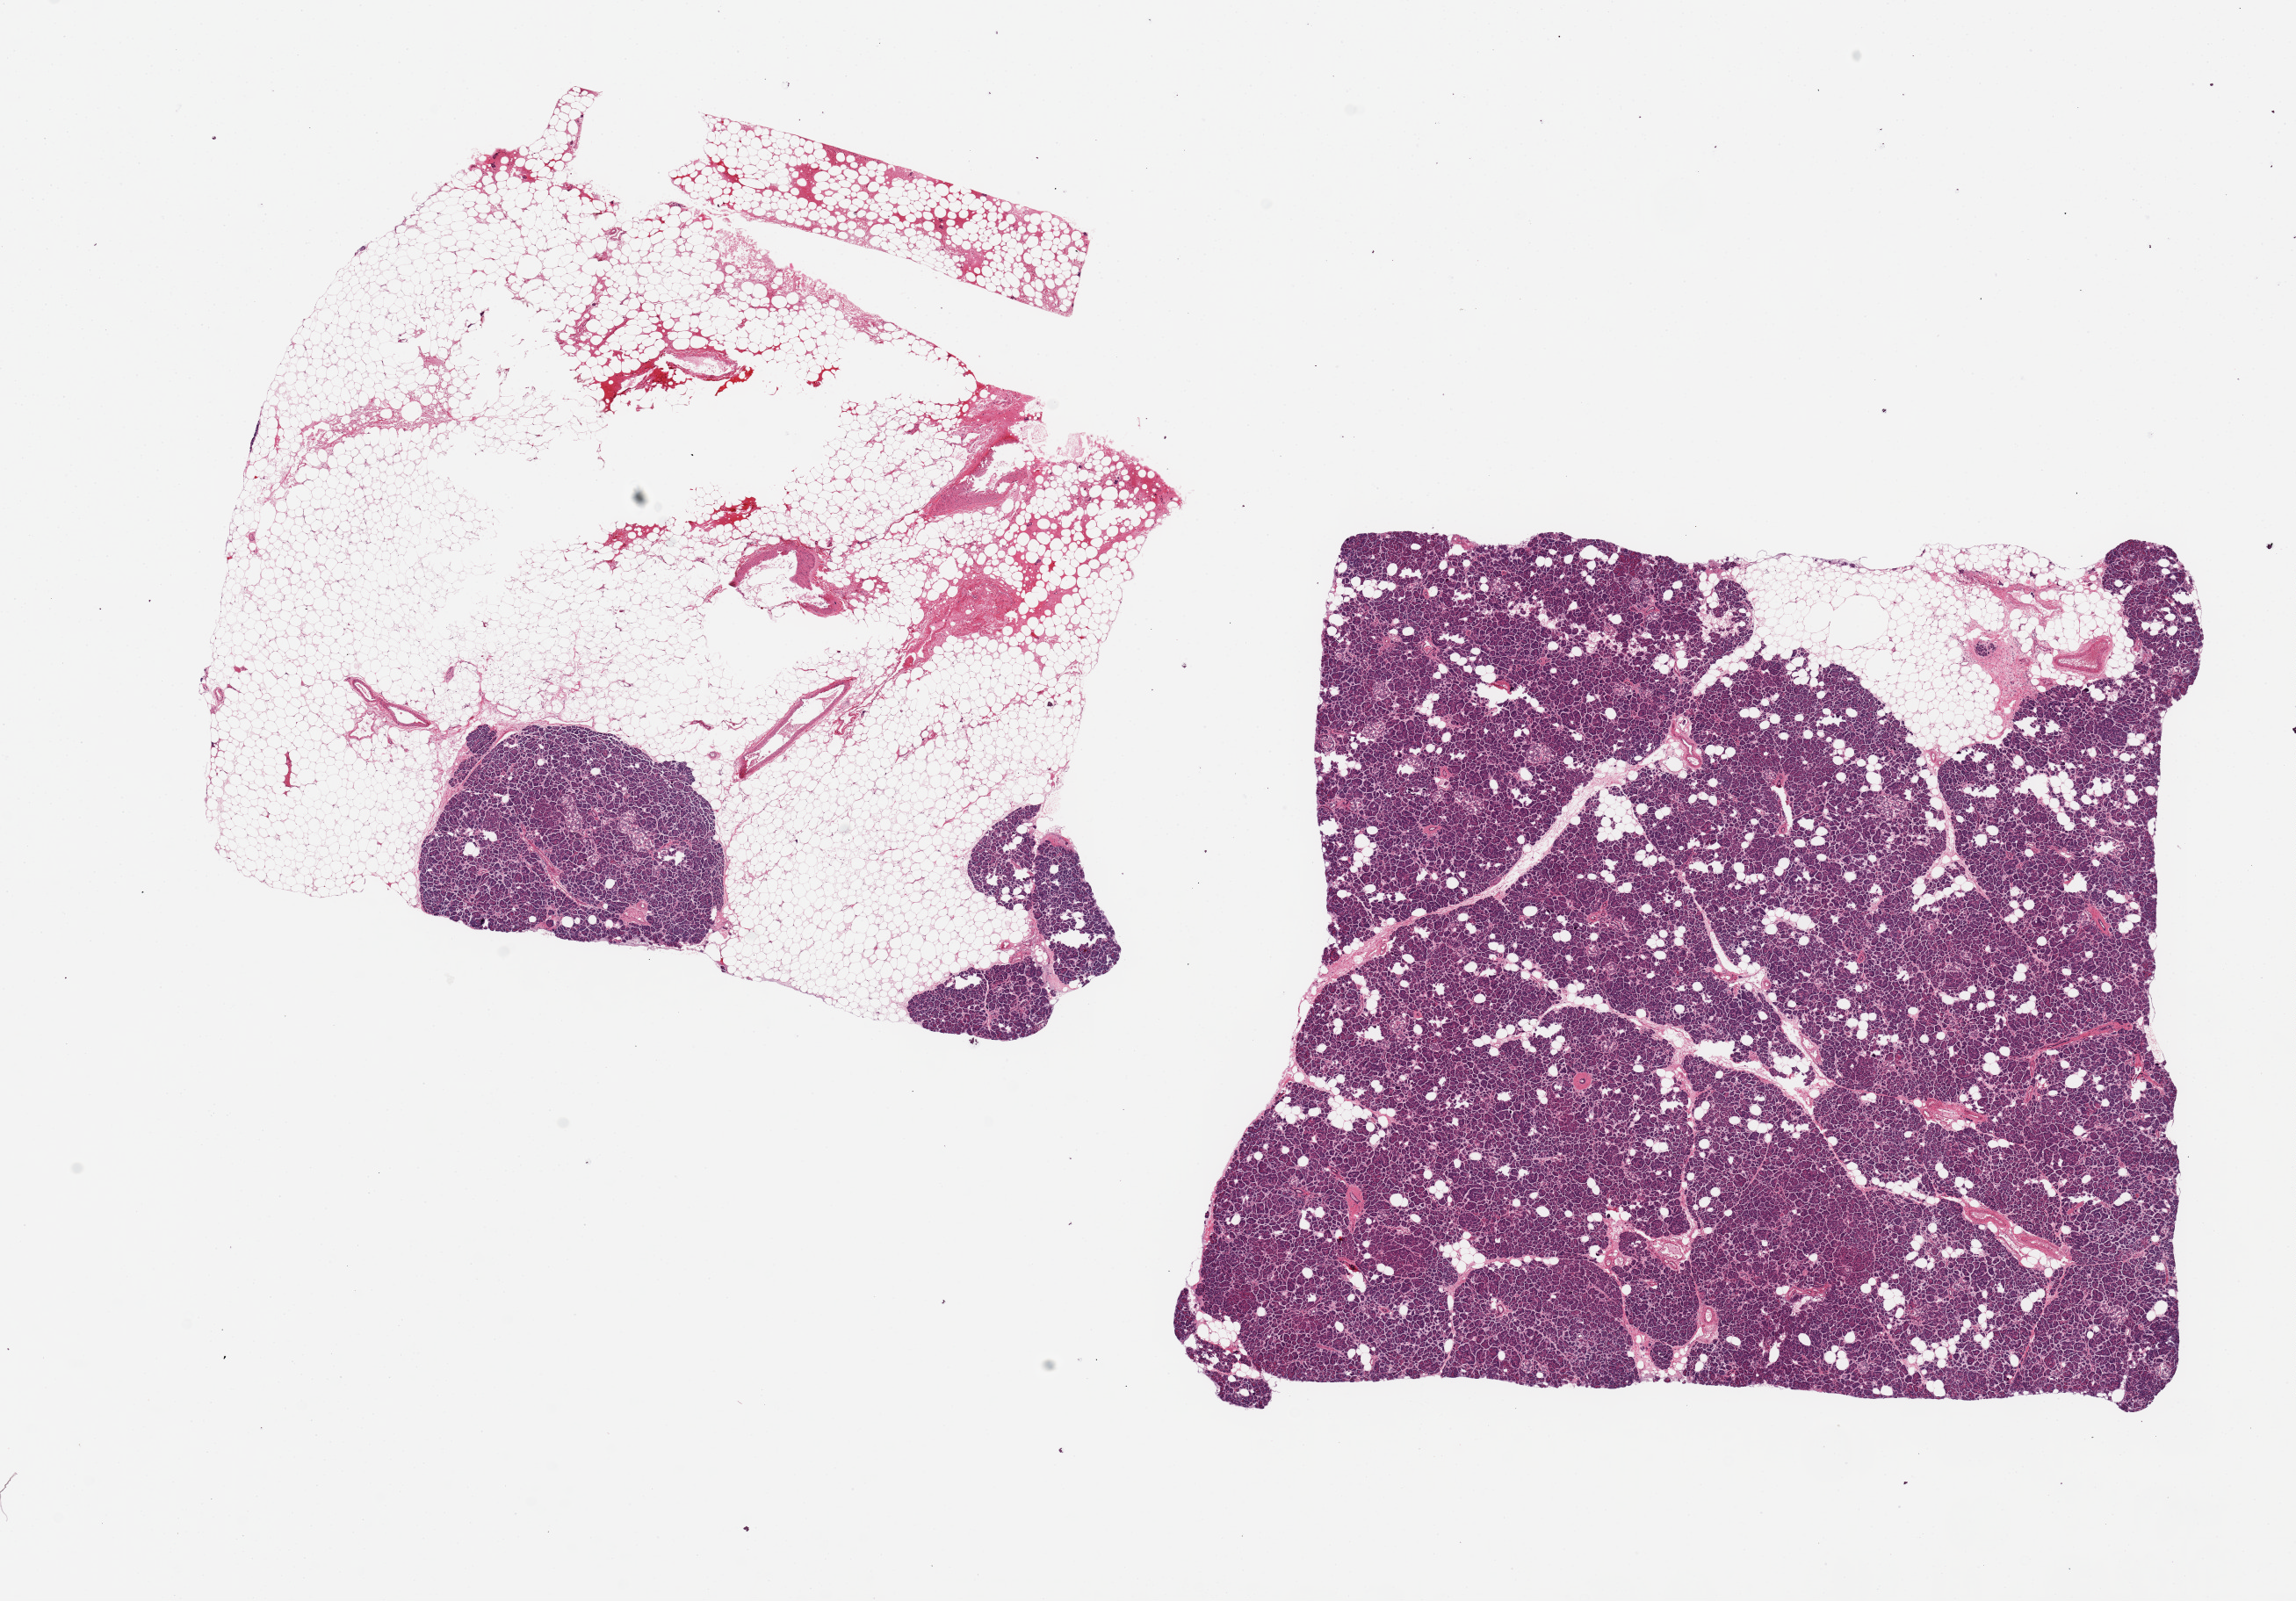
Haematoxylin and eosin whole-slide image, low-resolution overview of the scanned area, about 20.7 x 14.4 mm (slide scanned at 20x). Donor: male.
• specimen: PAXgene-fixed, paraffin-embedded tissue; section of pancreas (target tissue); tissue donor sample